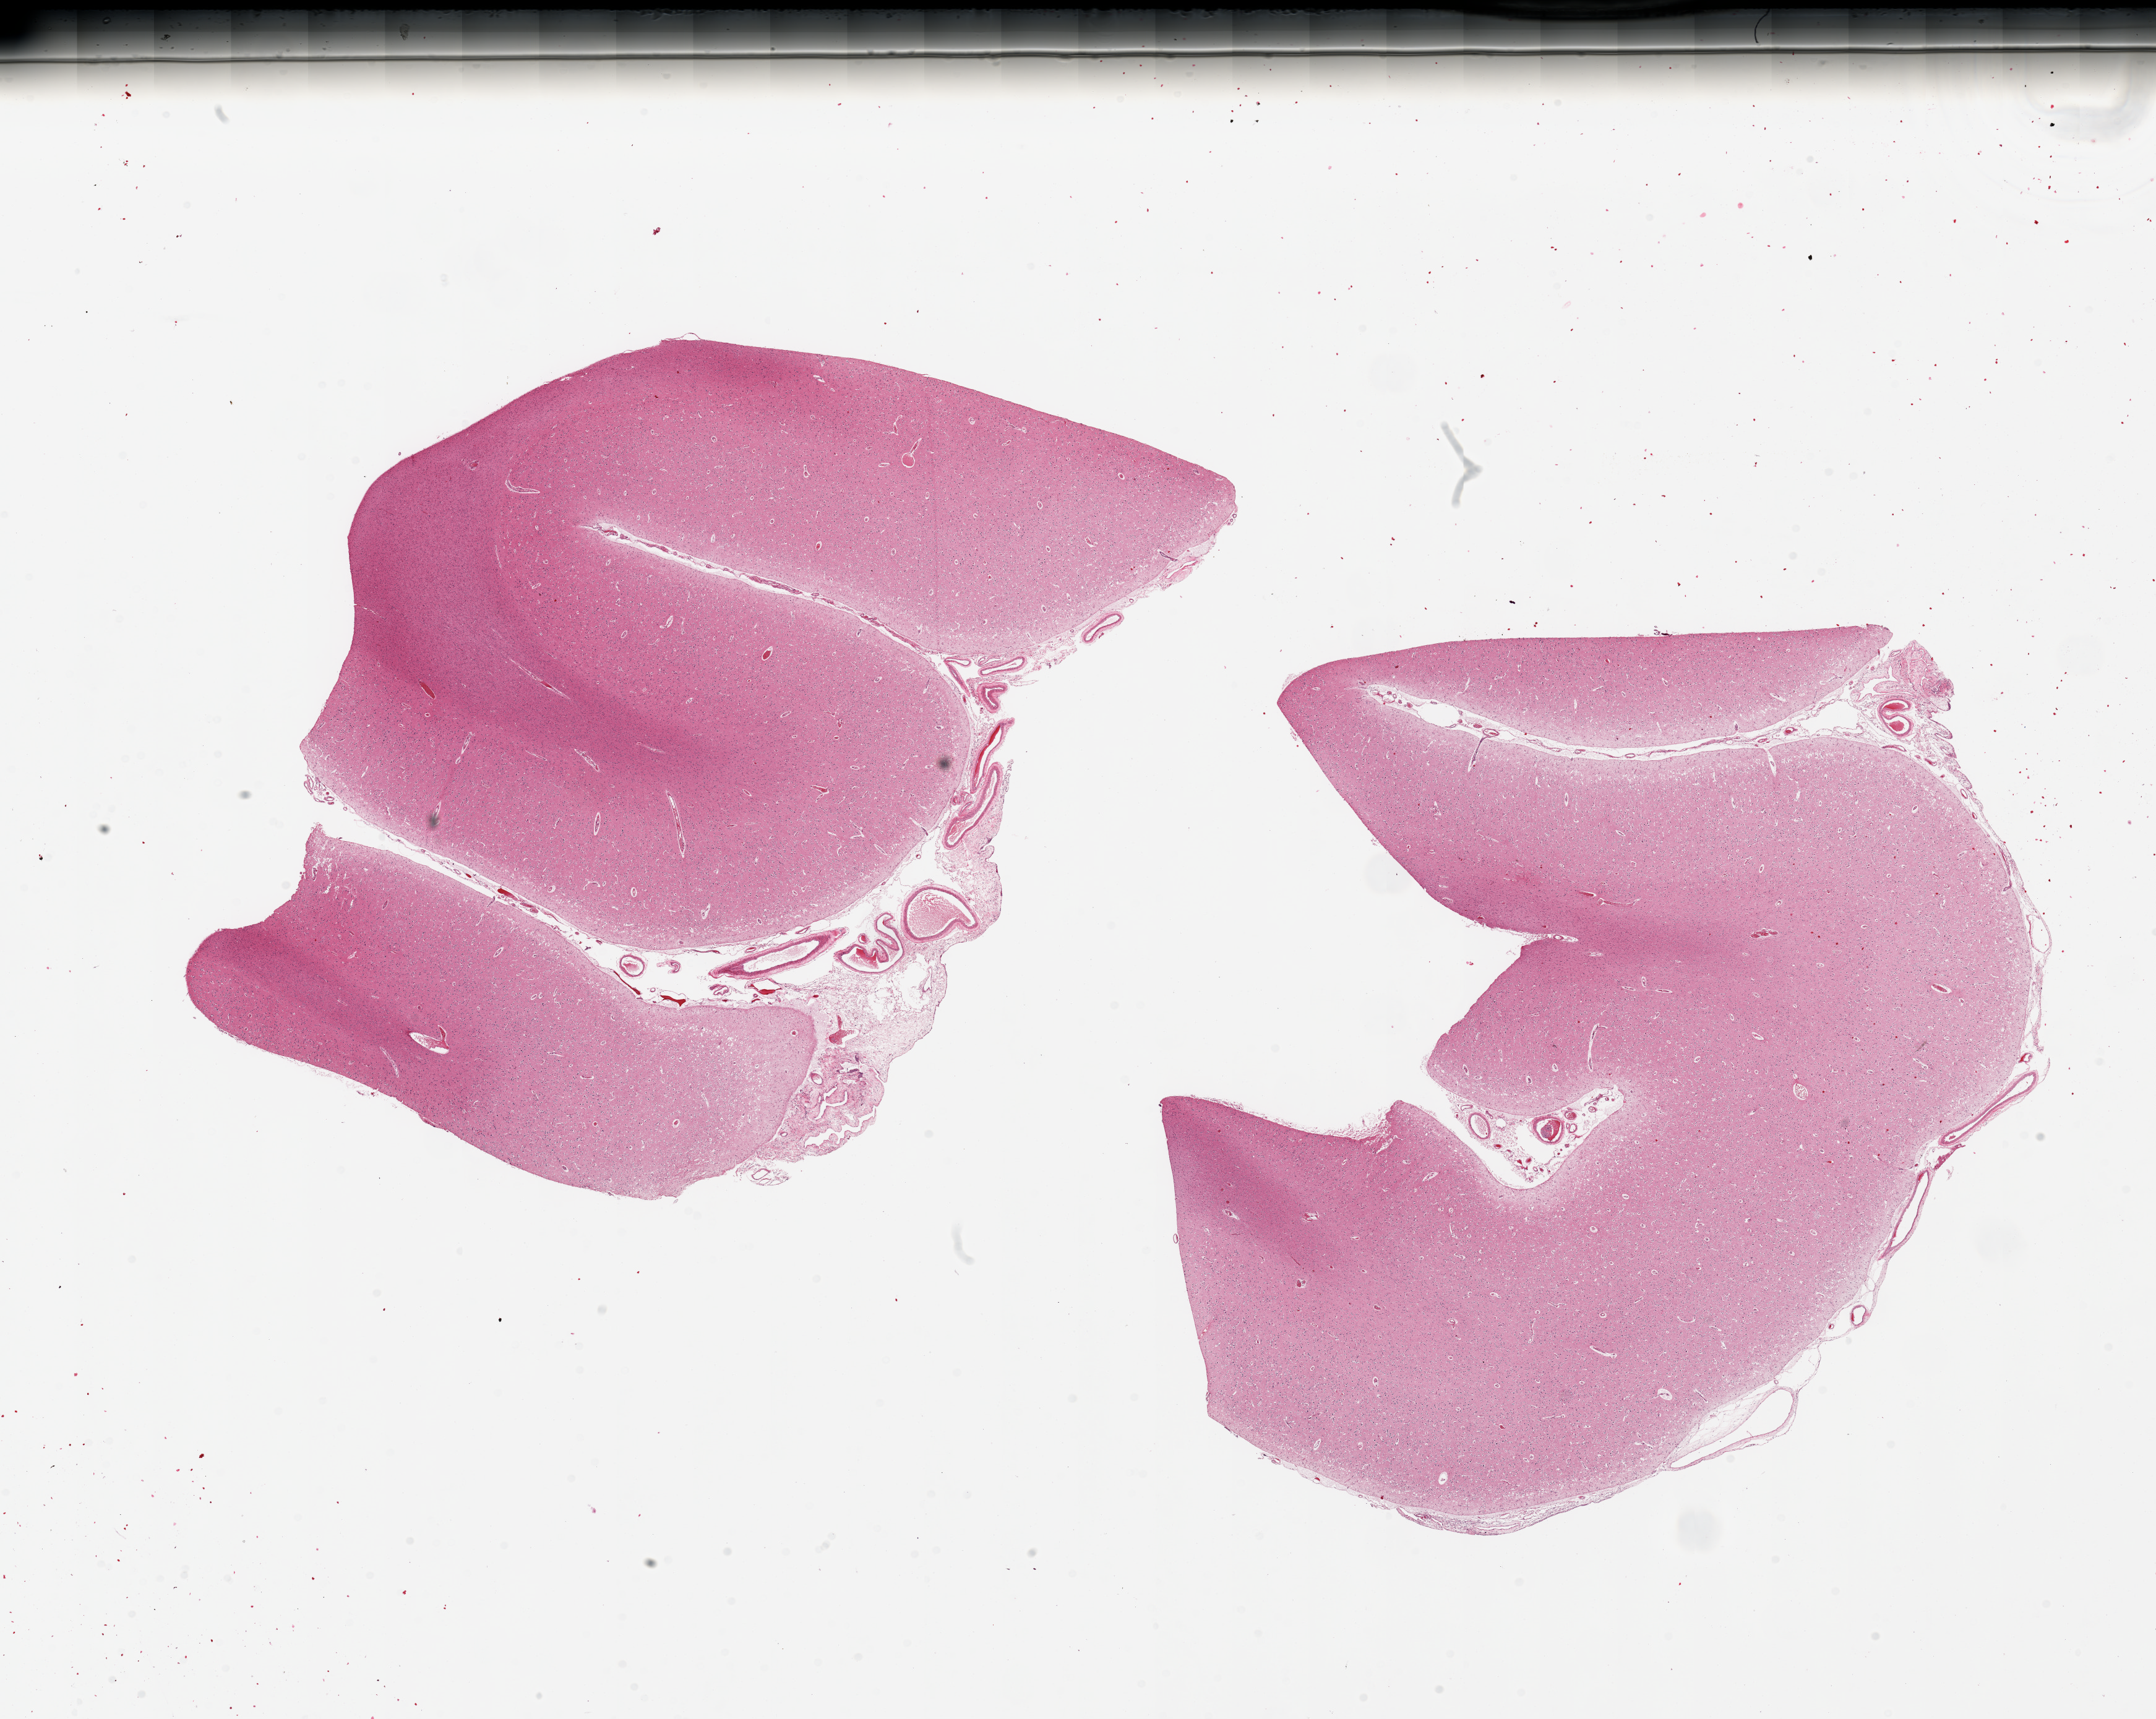
Digitized haematoxylin and eosin-stained section, brightfield, shown as a low-resolution overview of the whole scanned area (about 27.6 x 22.0 mm, acquisition: 20x scan), PAXgene-fixed paraffin-embedded (PFPE) section, target tissue: cerebral cortex, tissue donor sample. Donor: male.
Pathologist's review note for this sample: 2 pieces; meninges present.